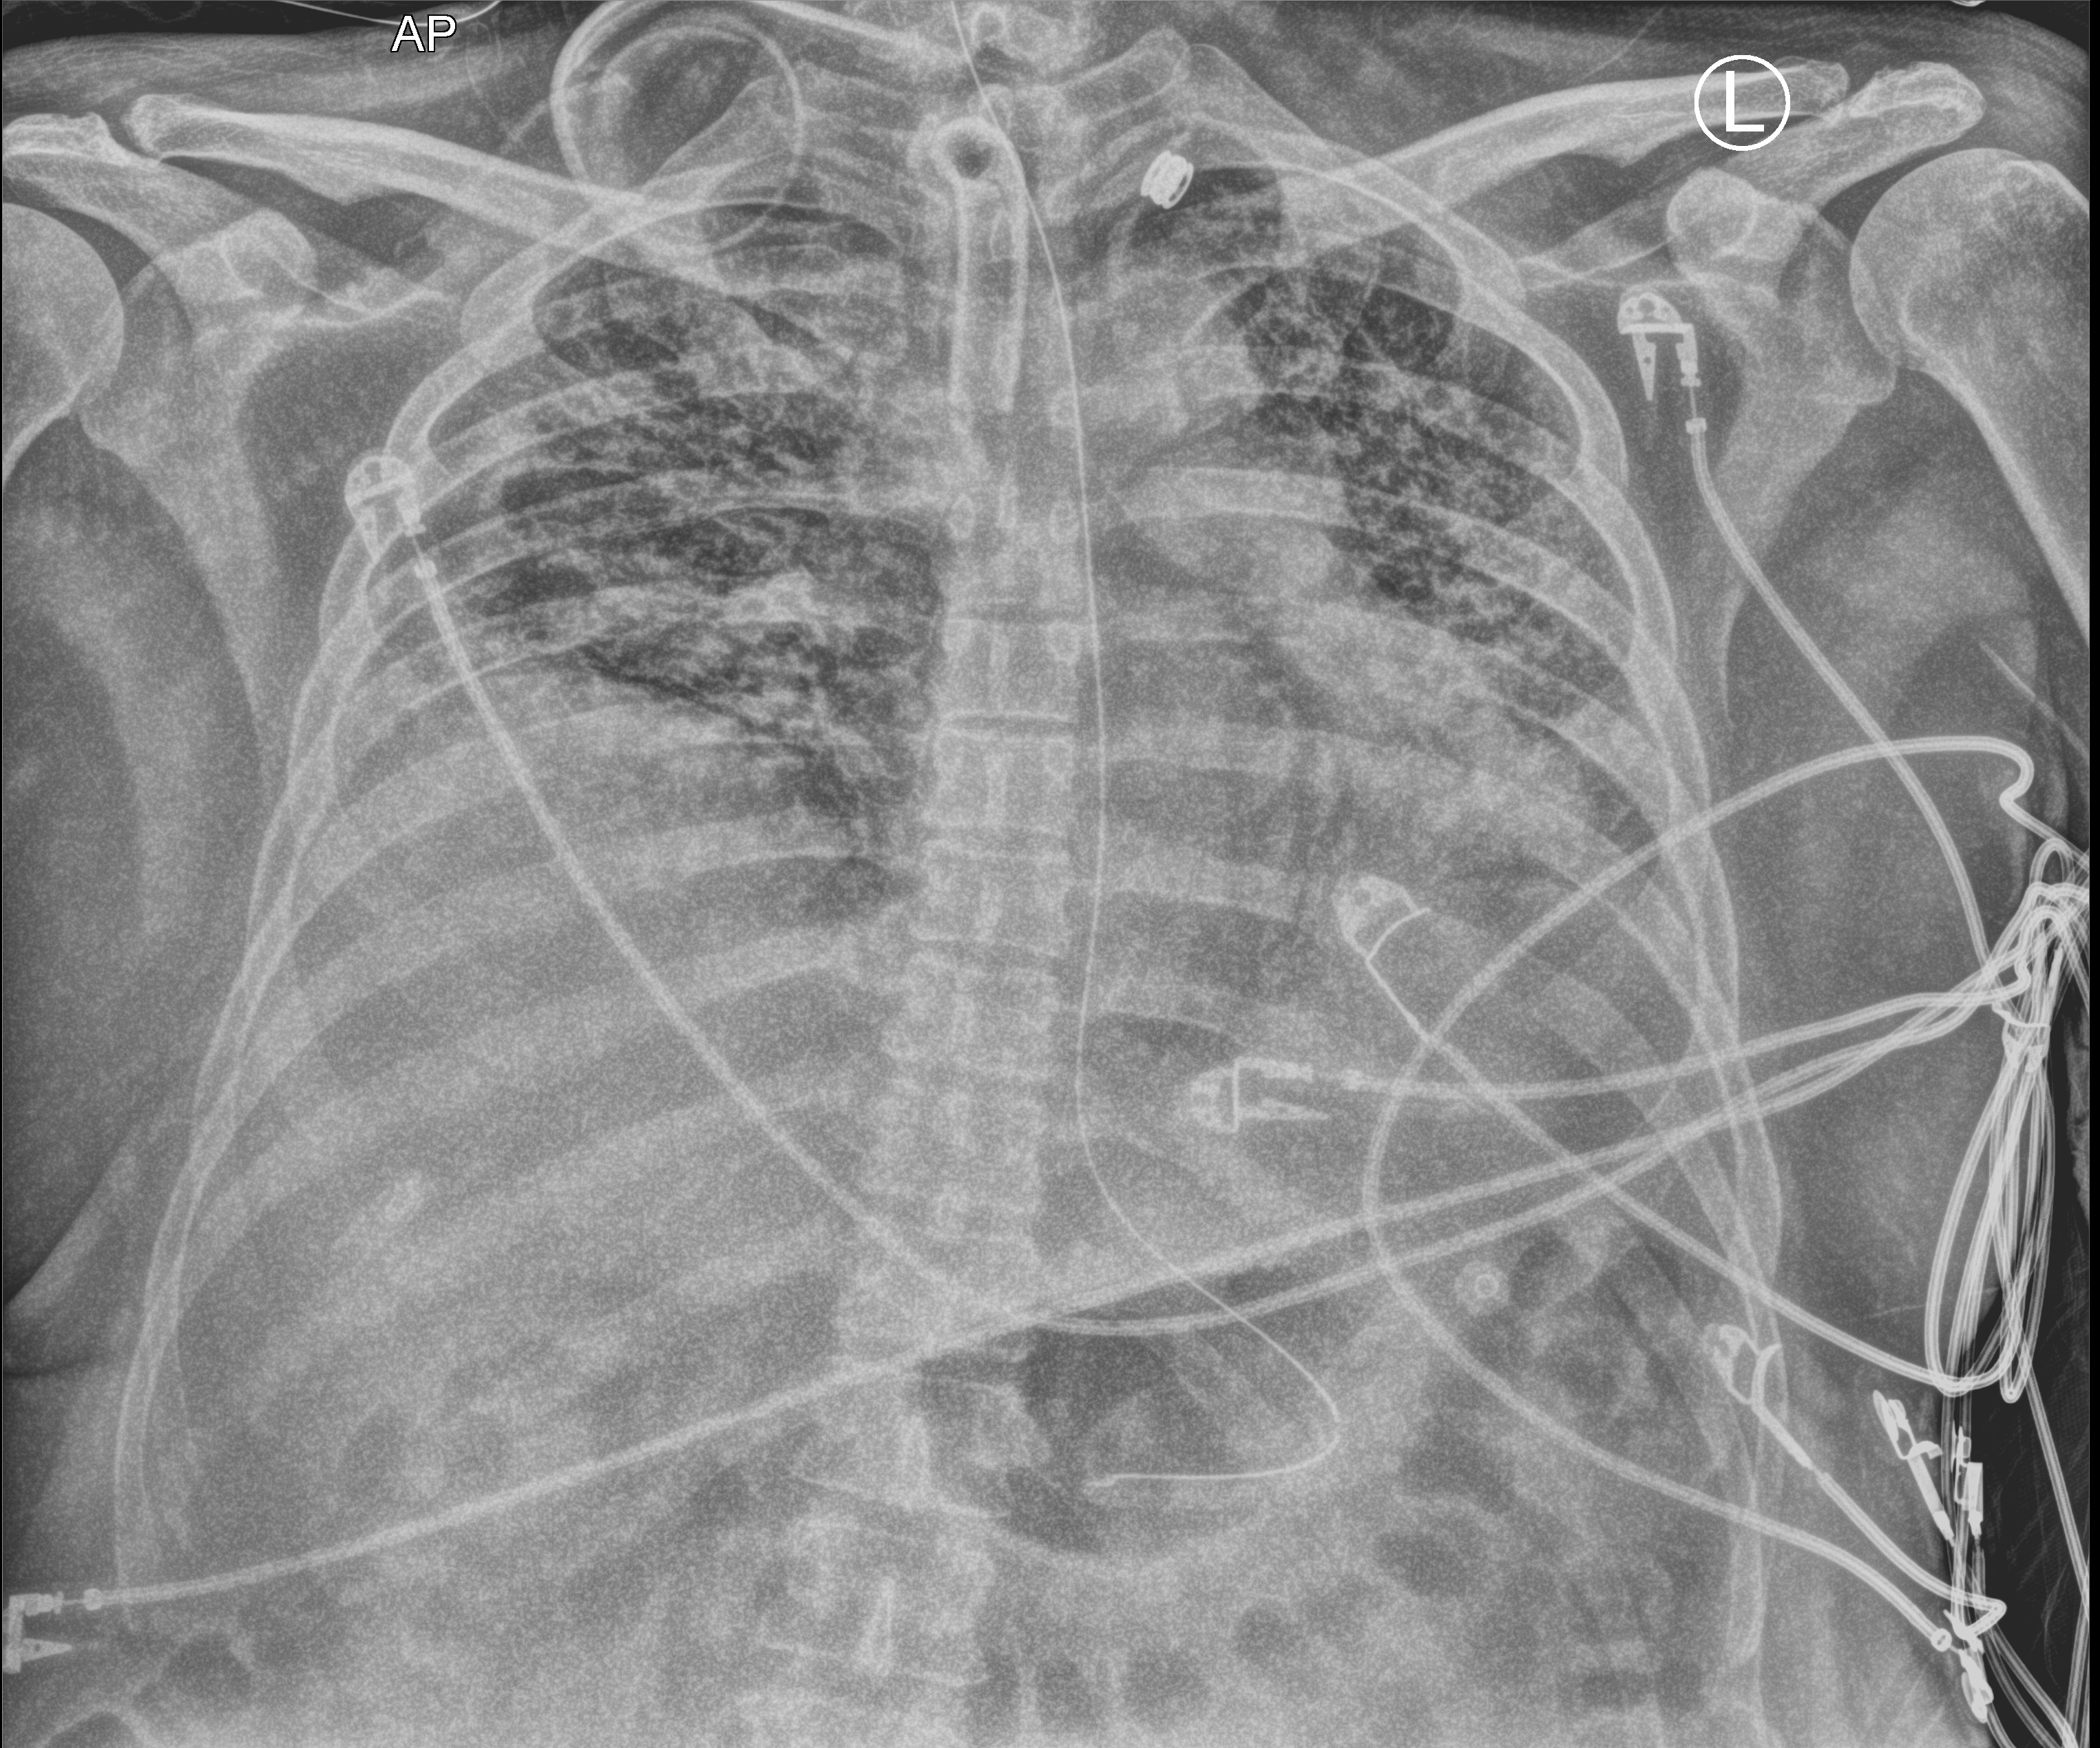
Bedside chest radiograph (computed radiography), anteroposterior (AP) projection. Male patient hospitalised with COVID-19, age 18–59 years.
From the hospital-stay record, not from the radiograph (when in the stay this image was taken is not recorded):
- mechanically ventilated during this hospital stay: yes
- admitted to intensive care during this hospital stay: yes